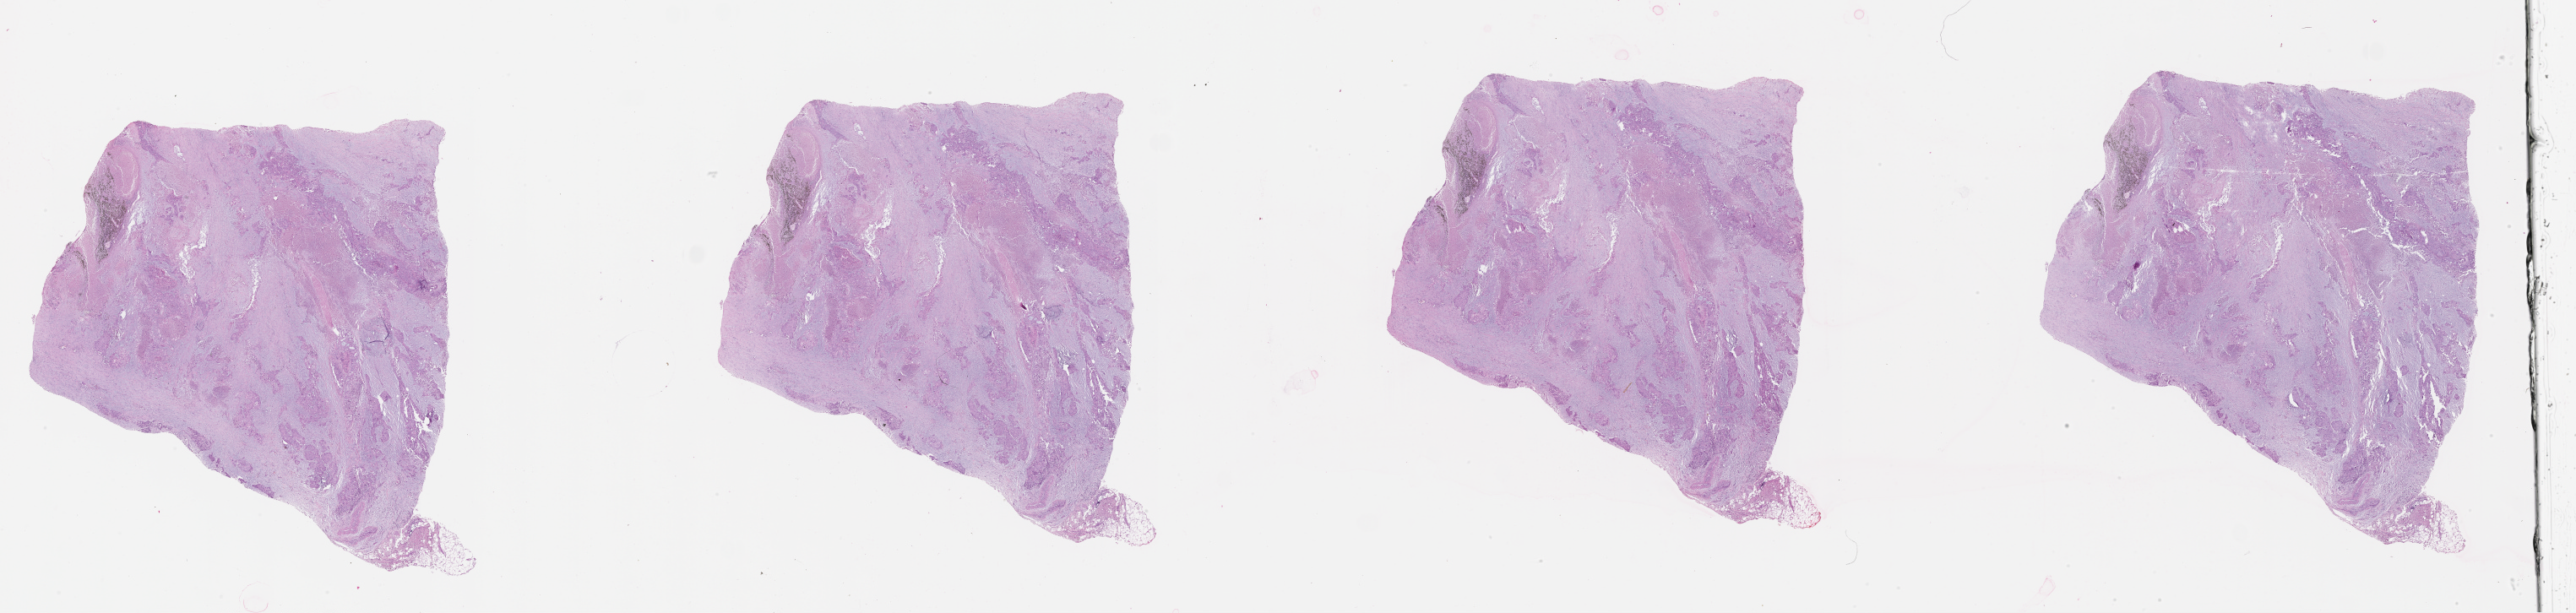
H&E whole-slide image, whole scanned area (about 49.1 x 11.7 mm, acquisition: 20x scan) shown as a low-resolution overview; lung, tumour tissue. 74-year-old male patient.
* patient diagnosis (cohort enrolment): squamous cell carcinoma (lung)